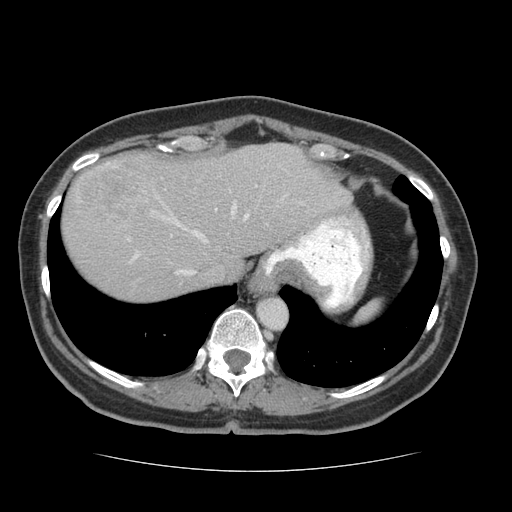
Contrast-enhanced abdominal CT (liver protocol), one axial slice. Slice 57 of 75 in the series (ordered by position). Reconstruction kernel STANDARD. Soft-tissue window (W 400 / L 40 HU). 512 × 512 image matrix, field of view 360 × 360 mm. From the clinical record (not read from this slice): diagnosis: hepatocellular carcinoma (patient treated with transarterial chemoembolisation; whether this scan precedes or follows treatment is not stated here); TNM stage (as recorded): Stage-I; Child-Pugh class: A; tumour differentiation: moderately differentiated.
Structures marked on this image (semi-automatic segmentation, software-assisted and operator-edited):
- abdominal aorta: bounding box [x1, y1, x2, y2] px = [258, 298, 287, 329]
- liver parenchyma outside the tumour (the mass and vessels are separate outlines, so this box may not span the whole liver): [62, 142, 352, 300]
- mass: [79, 160, 147, 224]
- liver vessels: [127, 185, 257, 275]